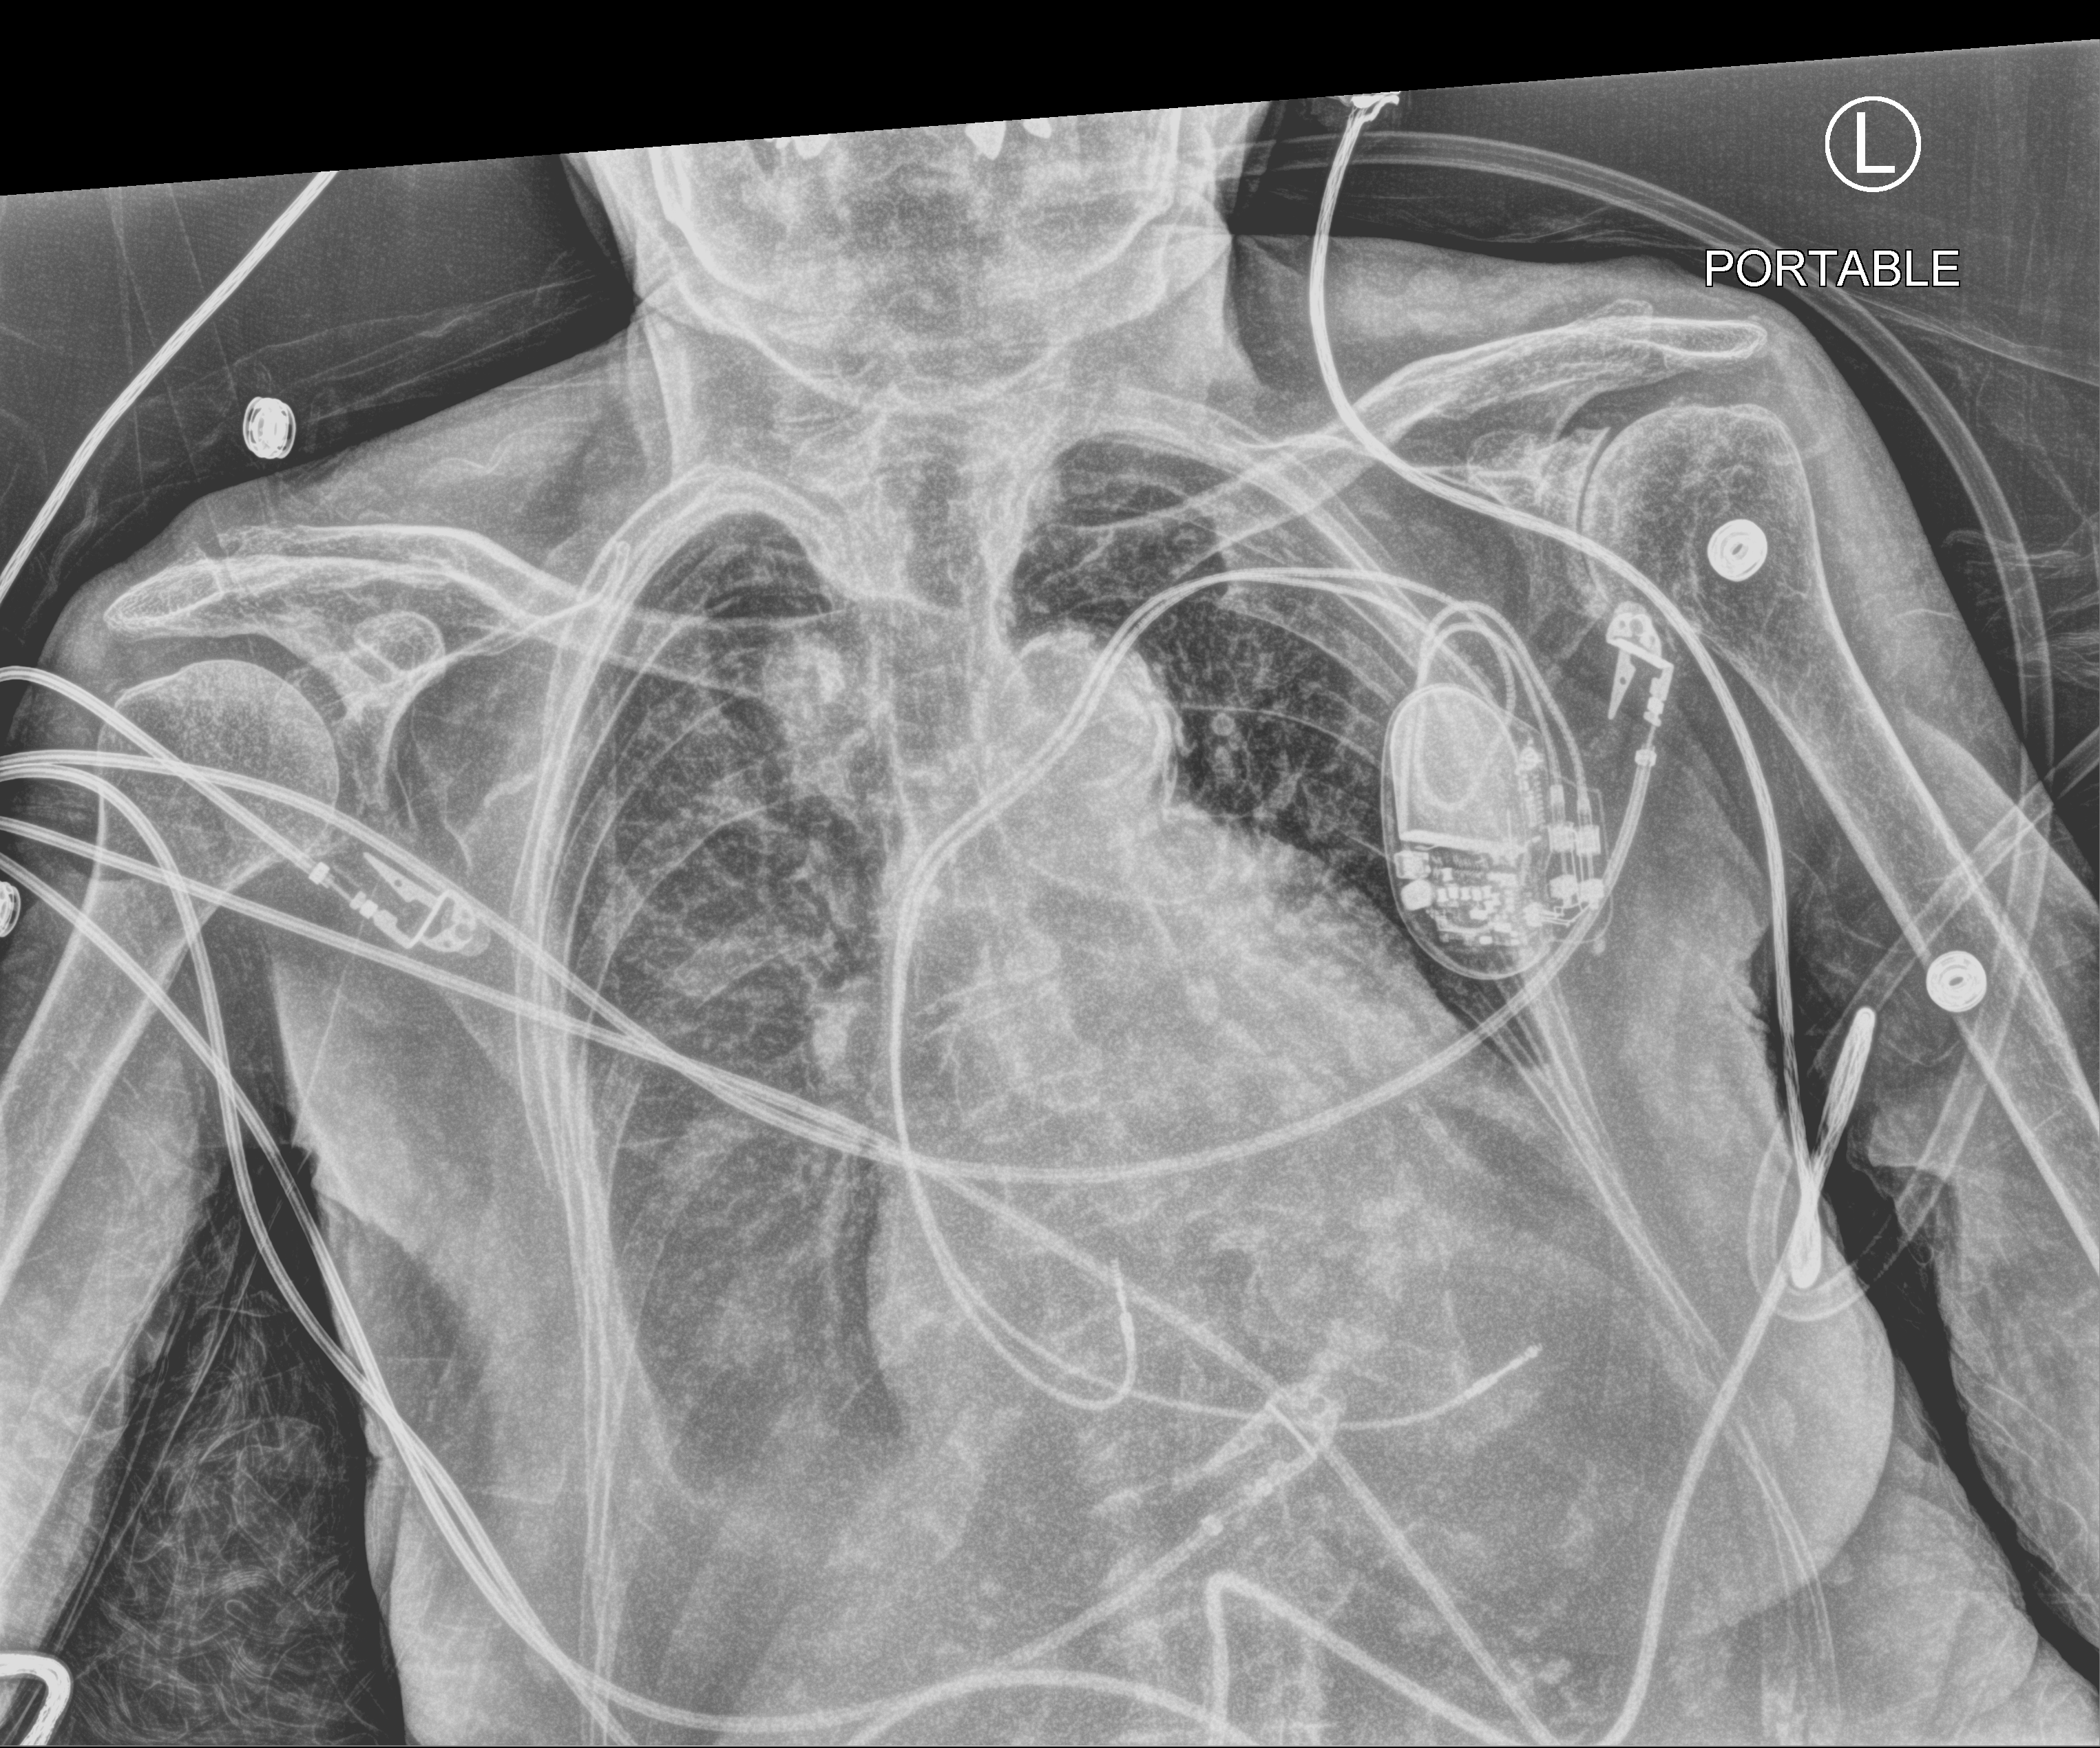
Portable chest radiograph, anteroposterior (AP) projection. Patient hospitalised with COVID-19; female, aged 75–90 years.
Hospital-stay facts (about this admission, not read from this image; timing relative to this image not recorded):
- length of hospital stay: 5 days
- mechanically ventilated during this hospital stay: no
- admitted to intensive care during this hospital stay: no